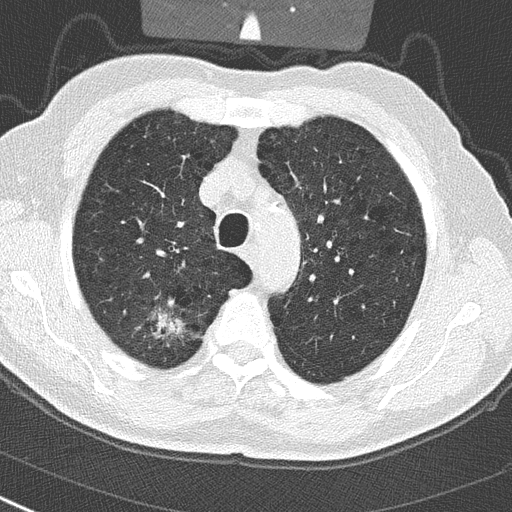
Axial slice from a low-dose chest CT screening exam. Baseline annual screen. Lung window (W 1500 / L -600 HU). 2 mm slice thickness. Lung (sharp) reconstruction kernel (B50f). Slice 69 of 290 in the series. 512 × 512 image matrix, field of view 300 × 300 mm. Male participant, aged 65 years at enrolment. Current smoker at enrolment.
Expert-annotated lung lesion, bounding box <130,299,197,359> (left, top, right, bottom; pixels). The exam's reader record, not a measurement of the box and not confirmed to be the same lesion: non-calcified nodule or mass ≥4 mm, right upper lobe, 24 × 19 mm, spiculated (stellate) margins, soft tissue attenuation.